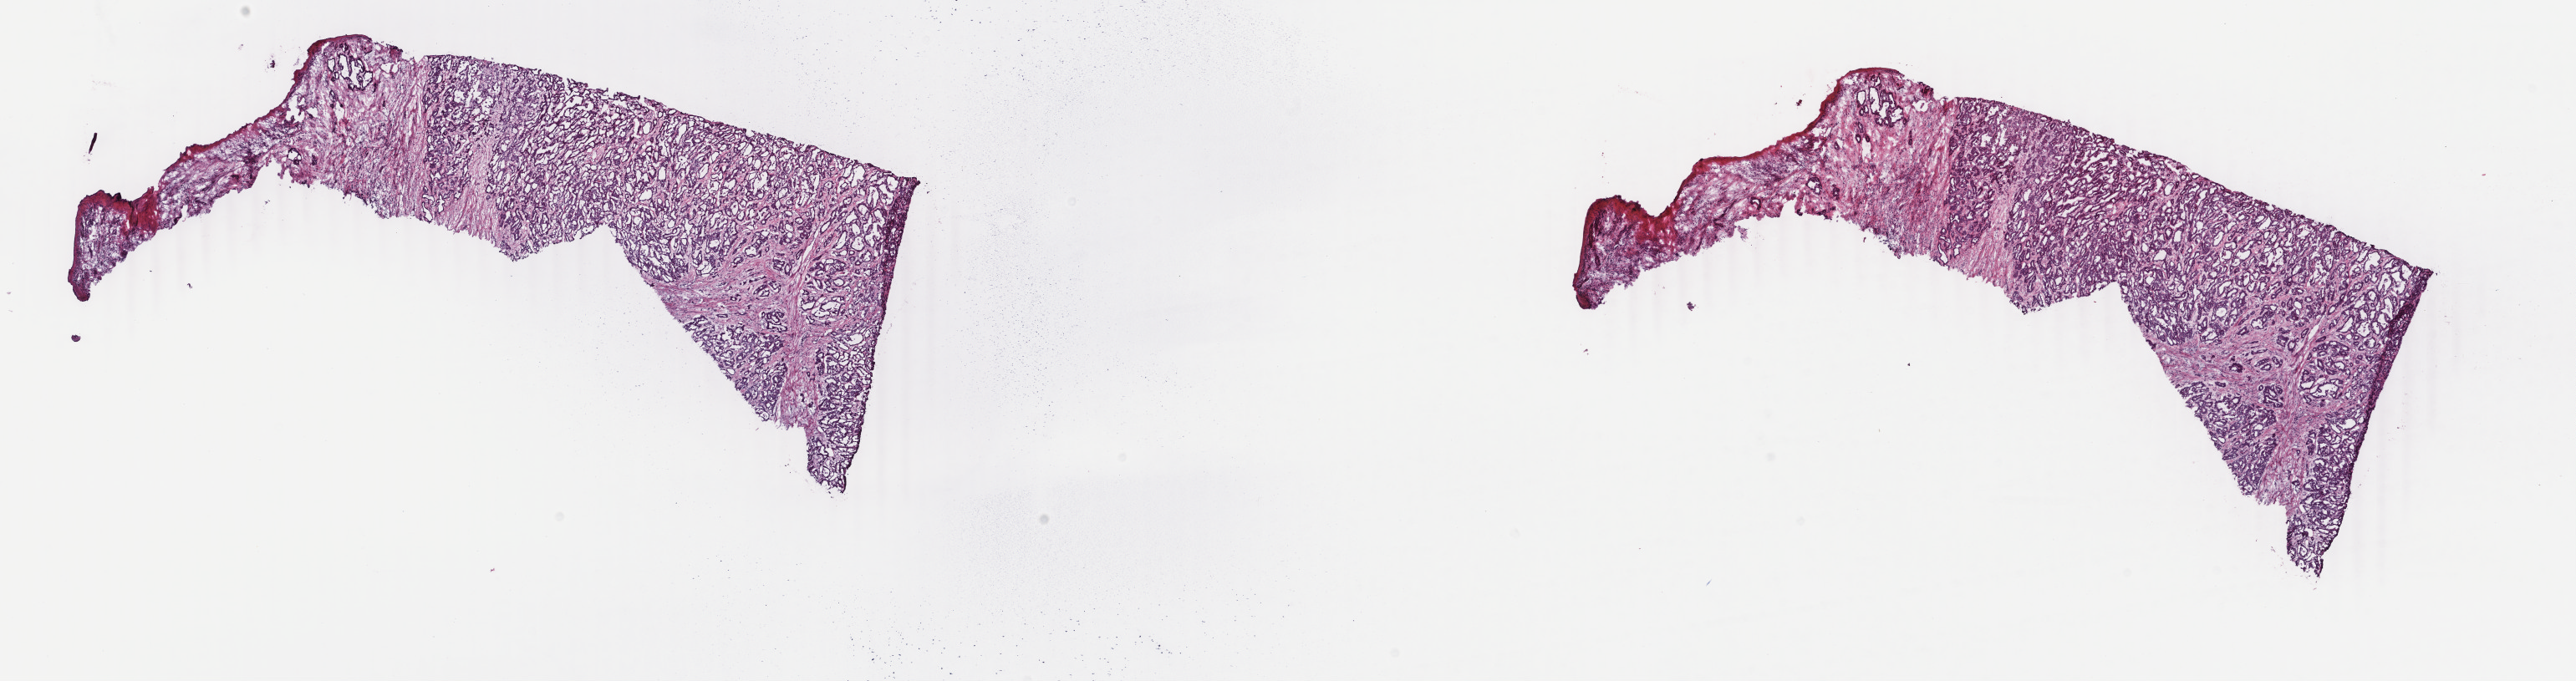
Whole-slide histology image, H&E-stained, shown as a low-resolution overview of the whole scanned area (about 24.5 x 6.5 mm, from a 40x scan); frozen section from the top of the tissue portion; liver, primary tumour sample. Female, age 72 years at initial diagnosis. Composition of this section per pathologist review: tumour cells 90%, tumour nuclei 80%, normal cells 0%, stromal cells 10%, necrosis 0%. Inflammatory infiltration, as recorded: lymphocyte infiltration 0%, monocyte infiltration 0%, neutrophil infiltration 0%.
Diagnosis: Hepatocellular carcinoma, NOS.